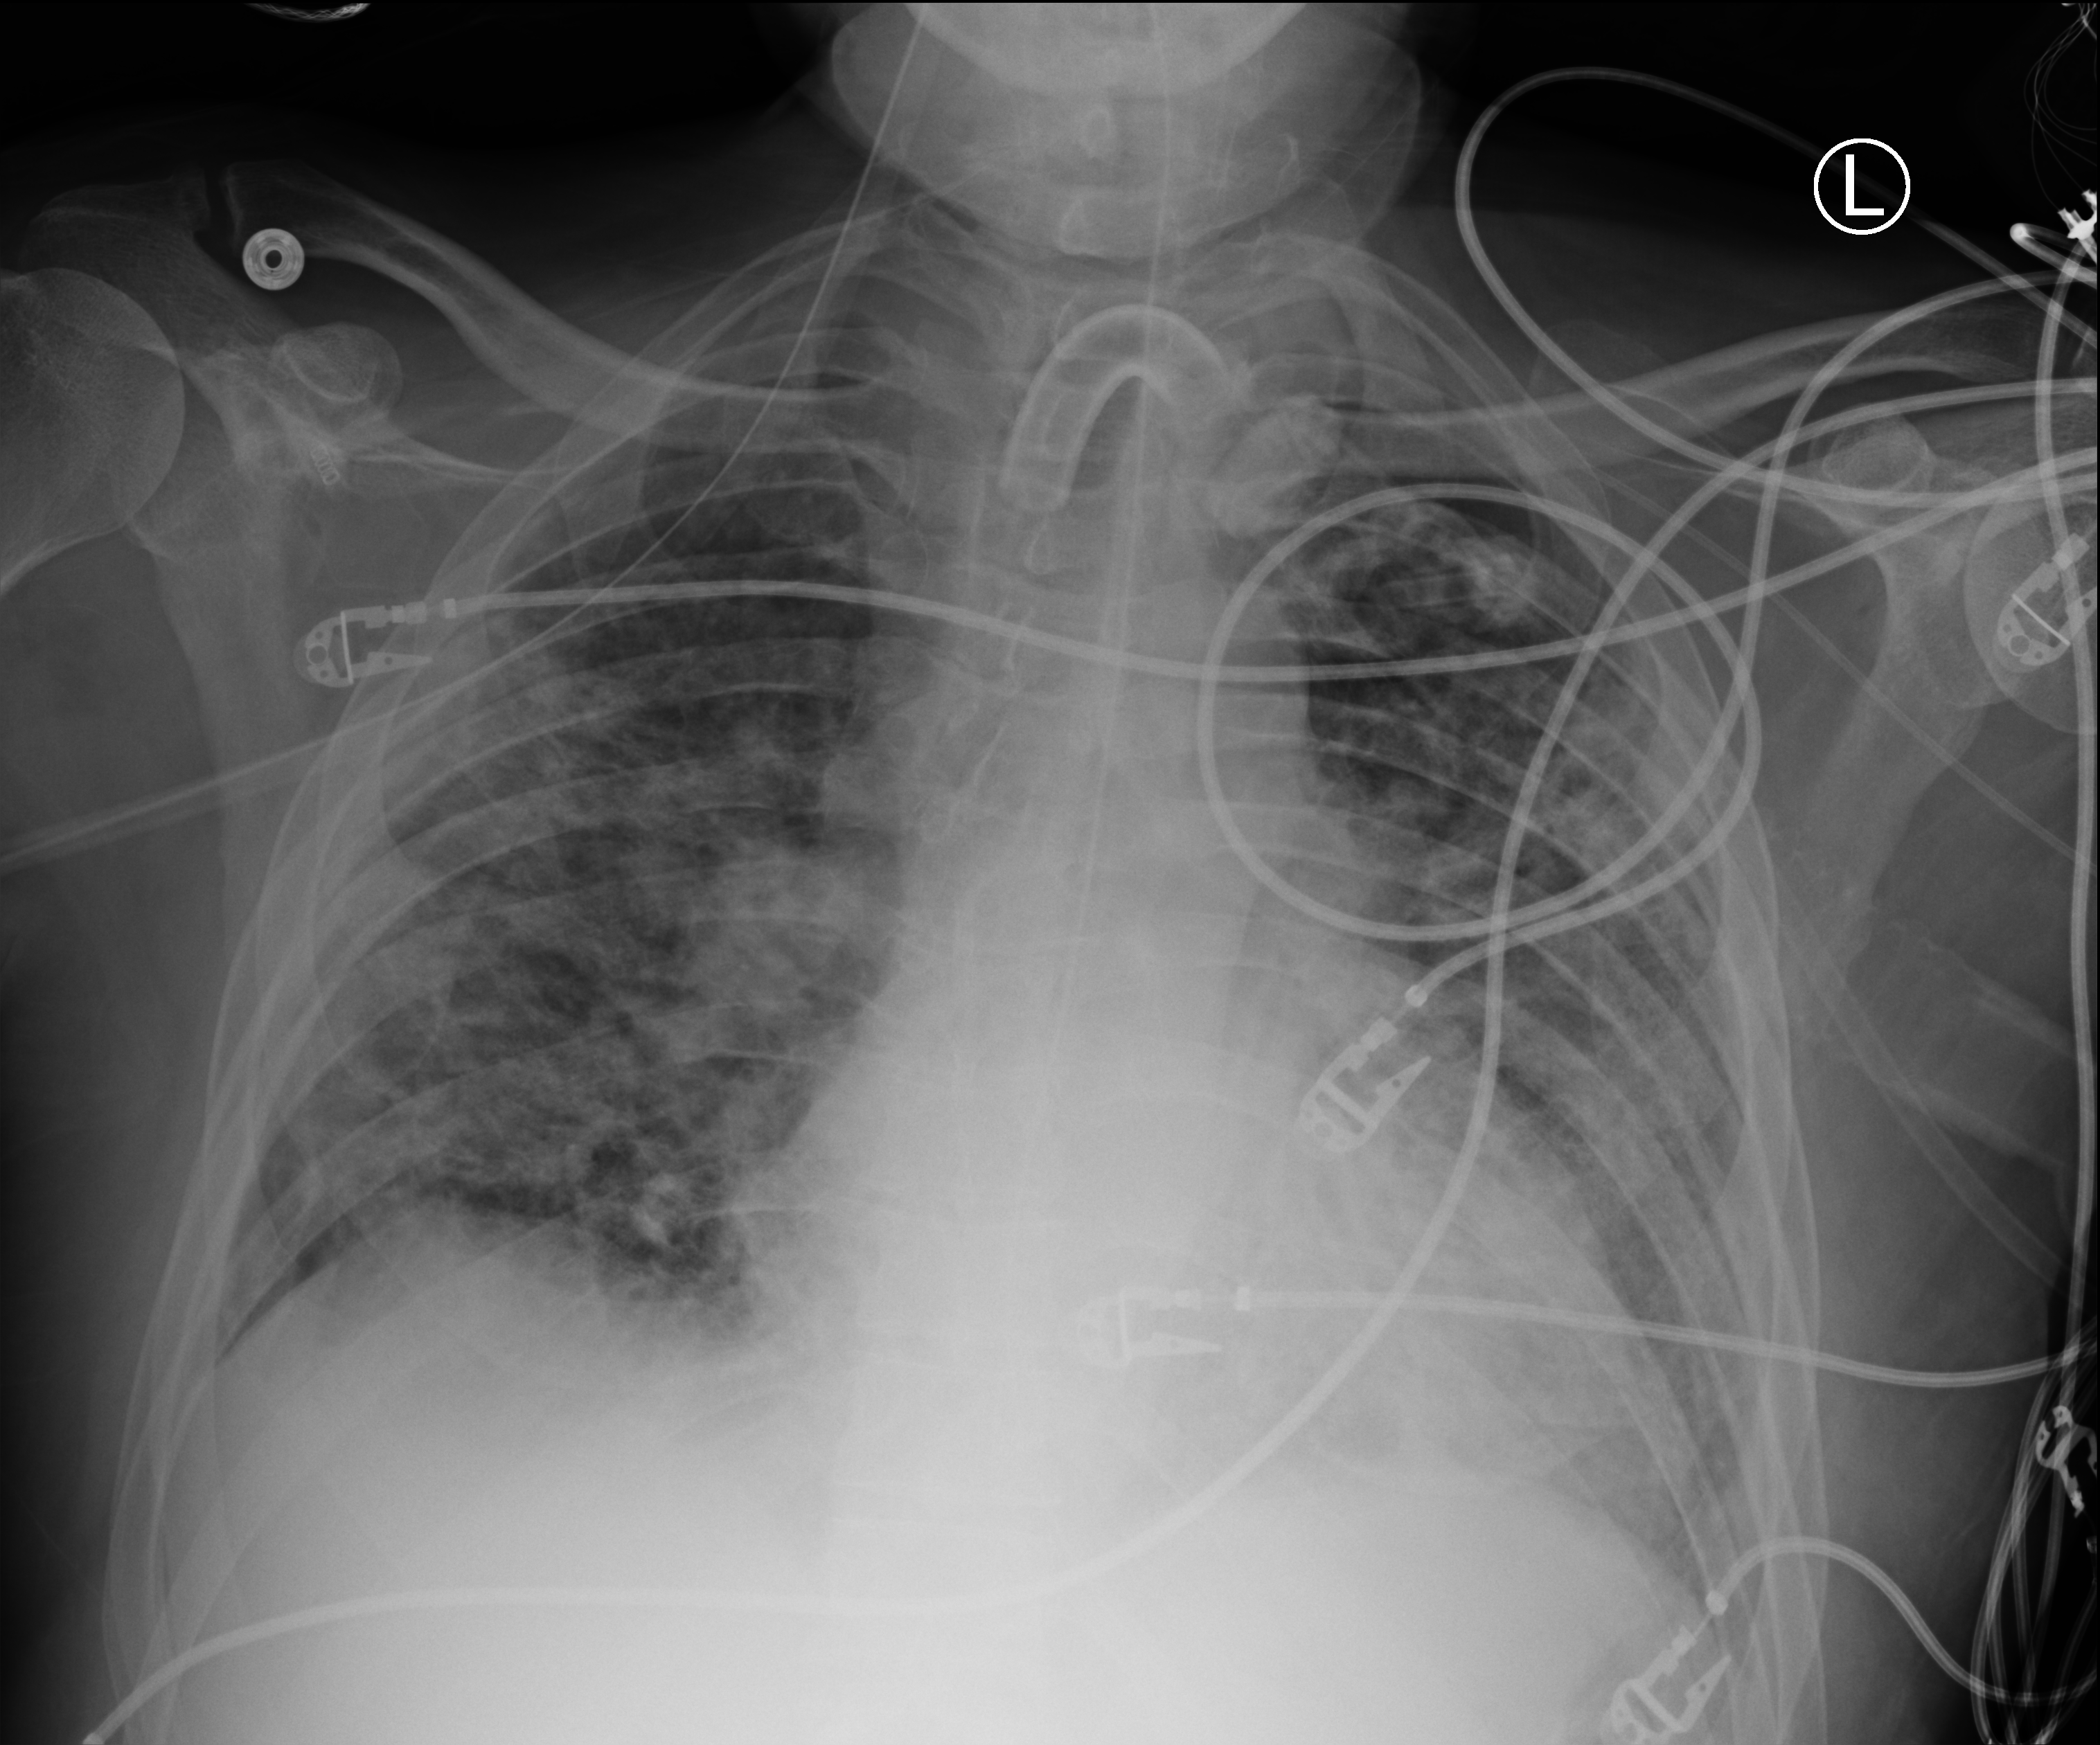
Portable chest radiograph; anteroposterior (AP) projection. Male patient hospitalised with COVID-19, age 18–59 years.
Hospital-stay facts (about this admission, not read from this image; timing relative to this image not recorded): mechanically ventilated during this hospital stay: yes; admitted to intensive care during this hospital stay: yes.